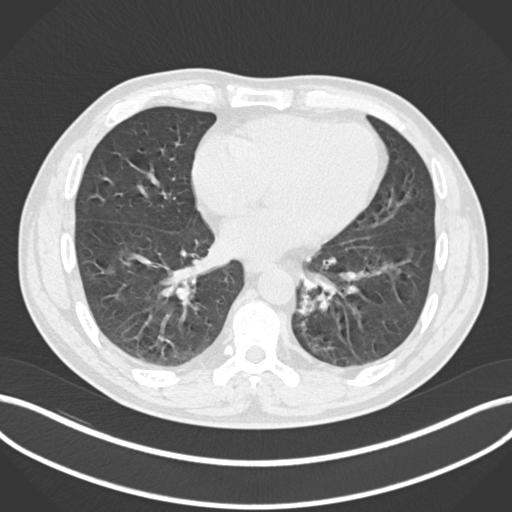
Chest CT, one axial slice. Position 73 of 223 along the scan axis. 120 kVp. Lung window (W 1500 / L -600 HU). 1 mm slice thickness. 512 × 512 image matrix, field of view 400 × 400 mm. Male patient, age 50 years. From the clinical record (not read from this slice): clinical TNM (as recorded): T2a N3 M0.
Outlined on this slice (bounding box drawn by a radiologist):
- lung tumour (recorded histology: squamous cell carcinoma): bounding box (x1, y1, x2, y2) in pixels: (294, 288, 315, 316)